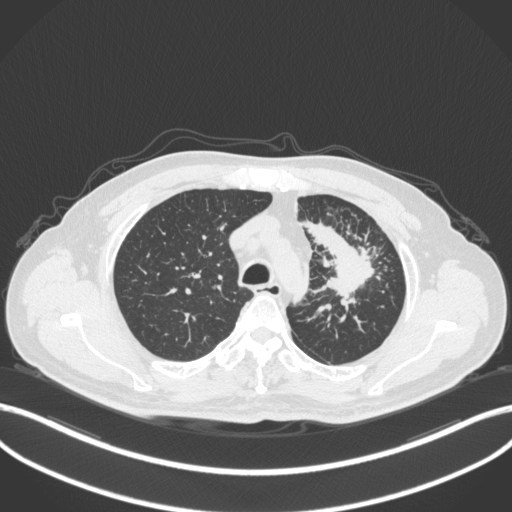
Chest CT, one axial slice. Position 274 of 386 along the scan axis. Reconstruction kernel B31f. 120 kVp. Lung window (W 1500 / L -600 HU). 512 × 512 image matrix, field of view 400 × 400 mm. Male patient, age 69 years. From the clinical record (not read from this slice): clinical TNM (as recorded): T2a N2 M0; histopathological grade: G2-3.
Structures marked on this image (bounding box drawn by a radiologist):
- lung tumour (recorded histology: adenocarcinoma): bounding box <298,218,377,299> (left, top, right, bottom; pixels)